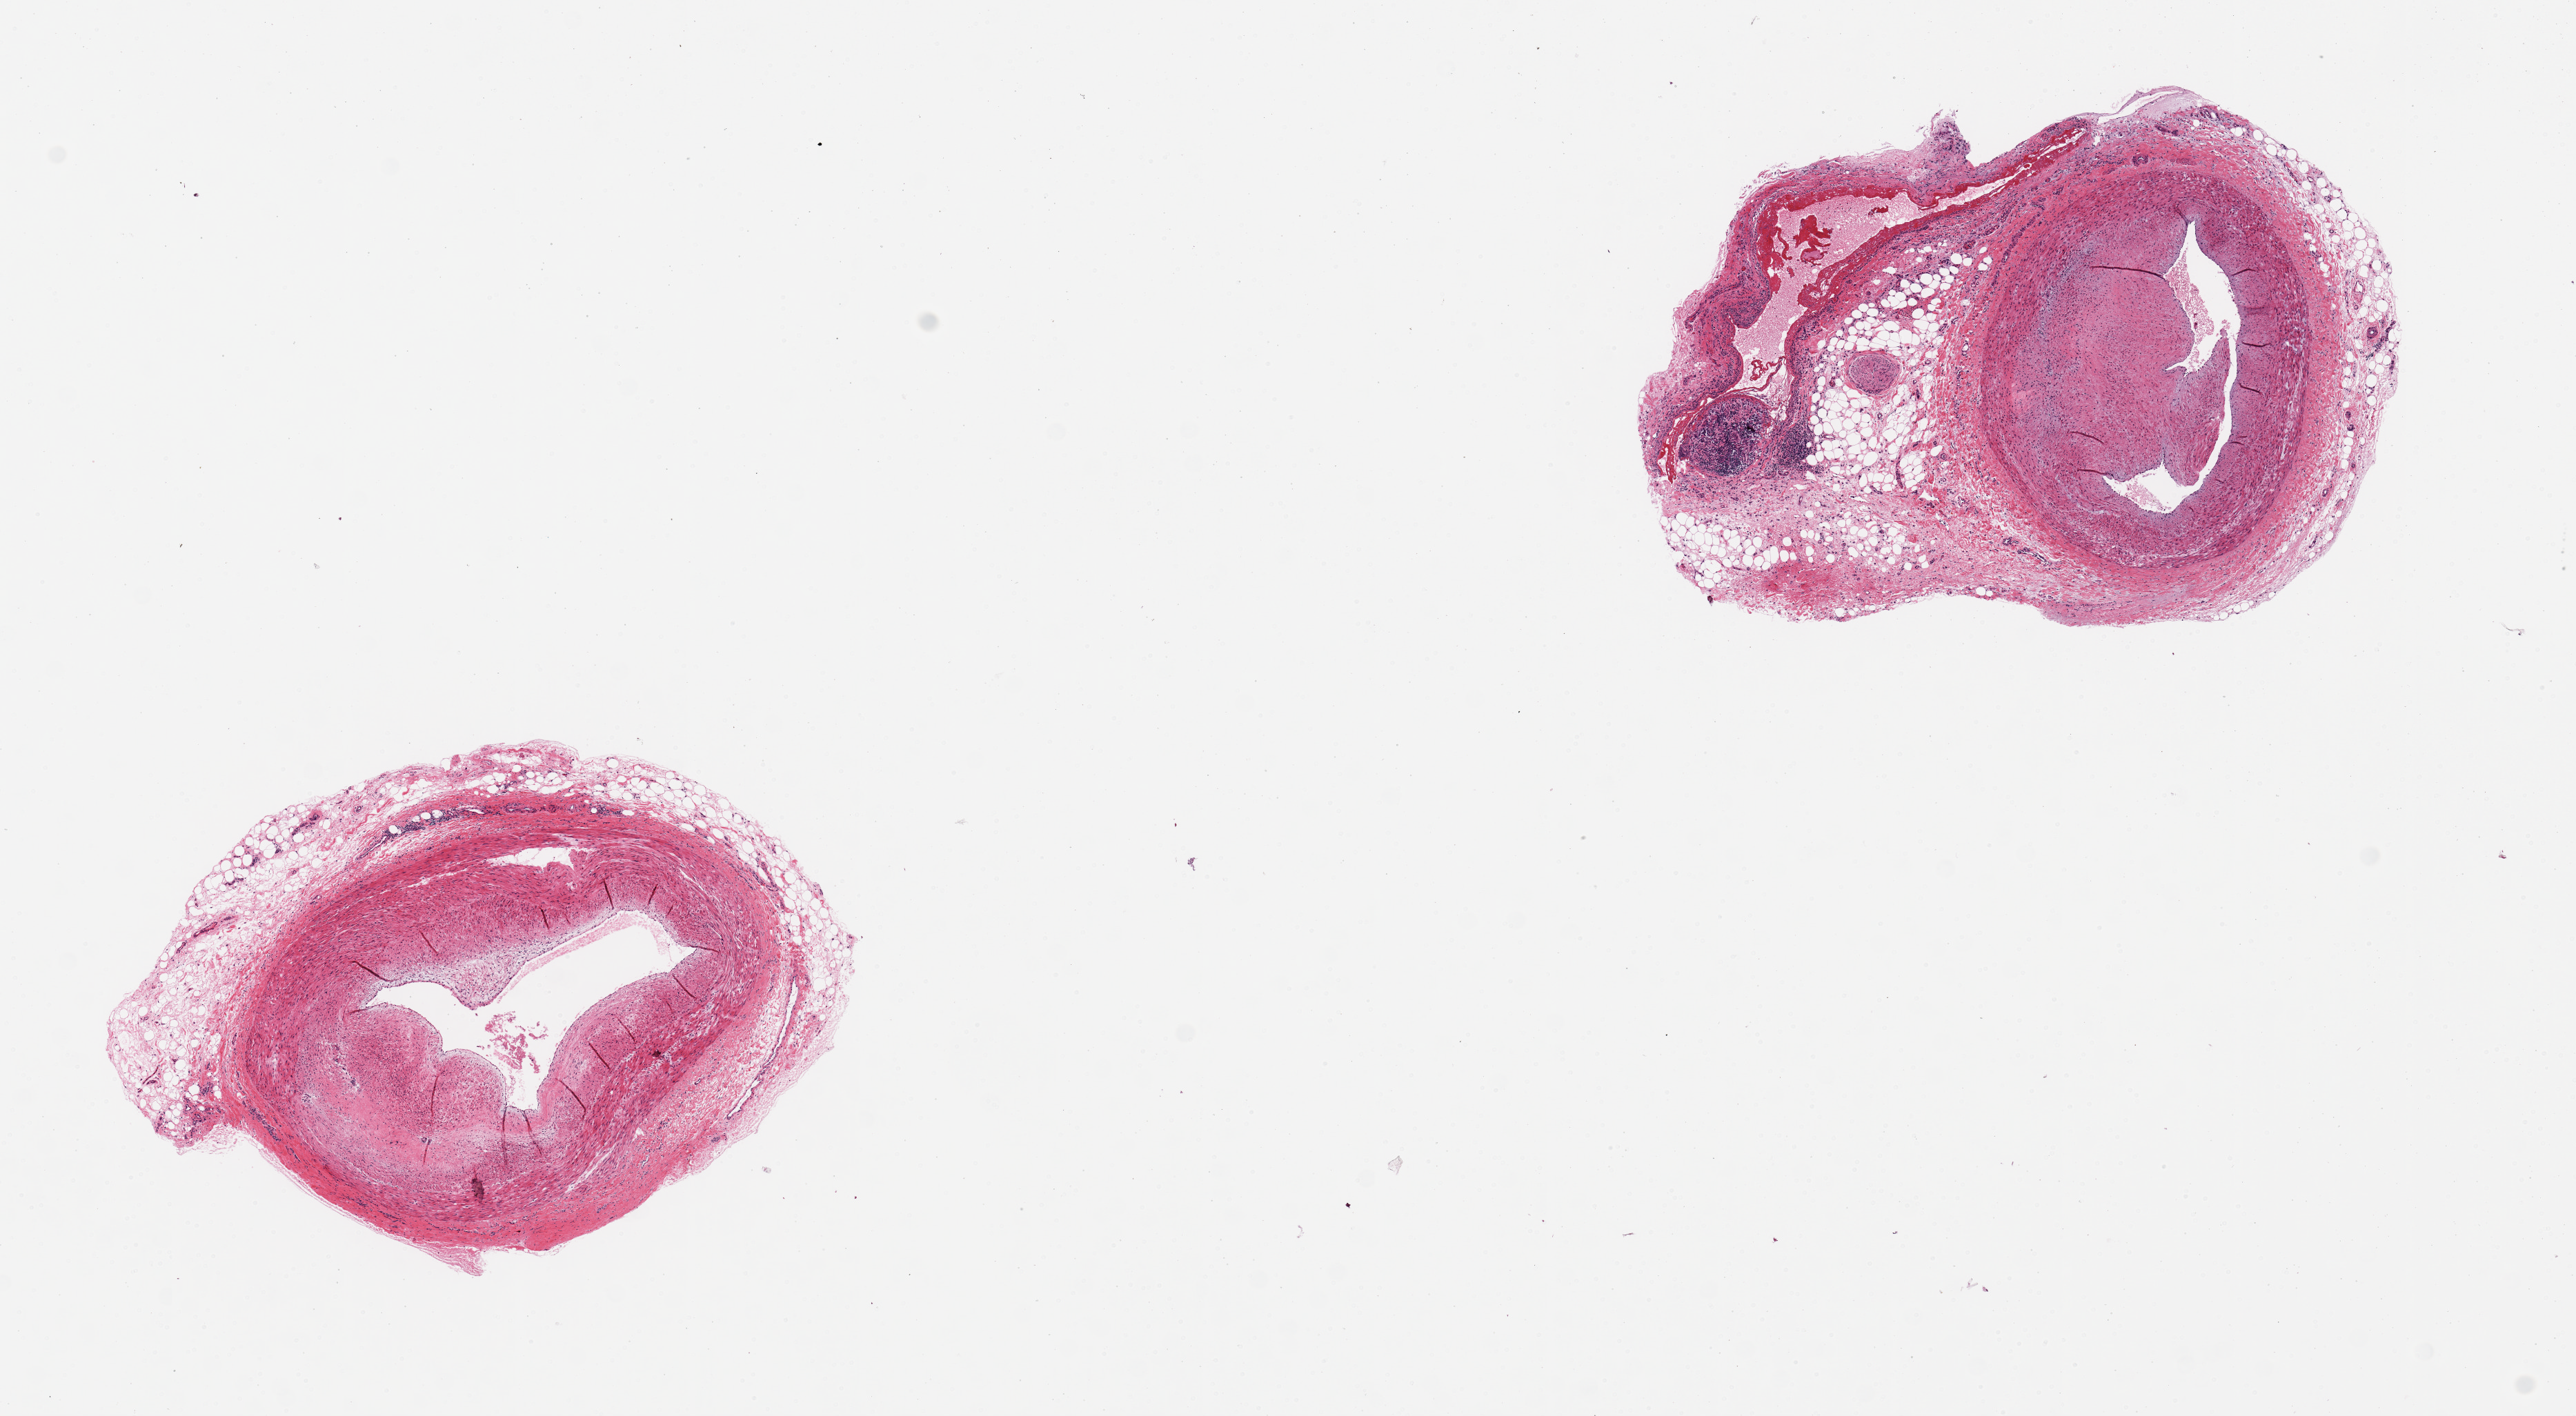
H&E whole-slide image, brightfield, a low-resolution overview of the entire scanned area, about 14.8 x 8.1 mm (from a 20x scan). PAXgene-fixed, paraffin-embedded tissue. Section of coronary artery (target tissue). Tissue donor sample. Donor sex: male.
• pathologist's review note for this sample: 2 pieces, subtotally occlusive atherosis; adherent fat up to ~2mm, unusually inflamed with necrobiosis